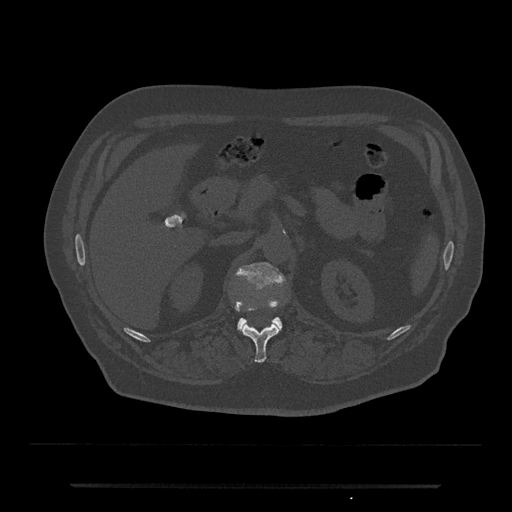
CT including the spine, one axial slice. Position 570 of 797 along the scan axis. Reconstruction kernel Br40s/3. Bone window (W 1800 / L 400 HU). 512 × 512 image matrix. Male patient, age 80 years. From the clinical record (not read from this slice): primary cancer: prostate.
Outlined on this slice (semi-automatic segmentation, software-assisted and operator-edited):
- L1 vertebra: bounding box <235,262,286,333> (left, top, right, bottom; pixels)
- T12 vertebra: <236,303,281,363>